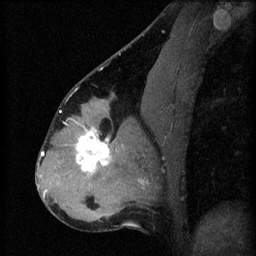
Breast MRI (dynamic contrast-enhanced), one sagittal slice; position 31 of 60 along the scan axis; 3 images stored at this slice position (order not interpretable as contrast timing); 1.5 T; TE 4.2 ms, TR 8.2 ms; 2.3 mm slice thickness; 256 × 256 image matrix, field of view 180 × 180 mm. Female patient, age 37 years.
Outlined on this slice (semi-automatic segmentation, software-assisted and operator-edited):
- analysis volume of interest (the breast-tissue region the enhancement analysis was run in; not a lesion): bounding box [x1, y1, x2, y2] px = [67, 120, 122, 179]
- tumour enhancement mask (voxels above the 70 % enhancement threshold inside the analysis volume of interest): [75, 128, 110, 173]